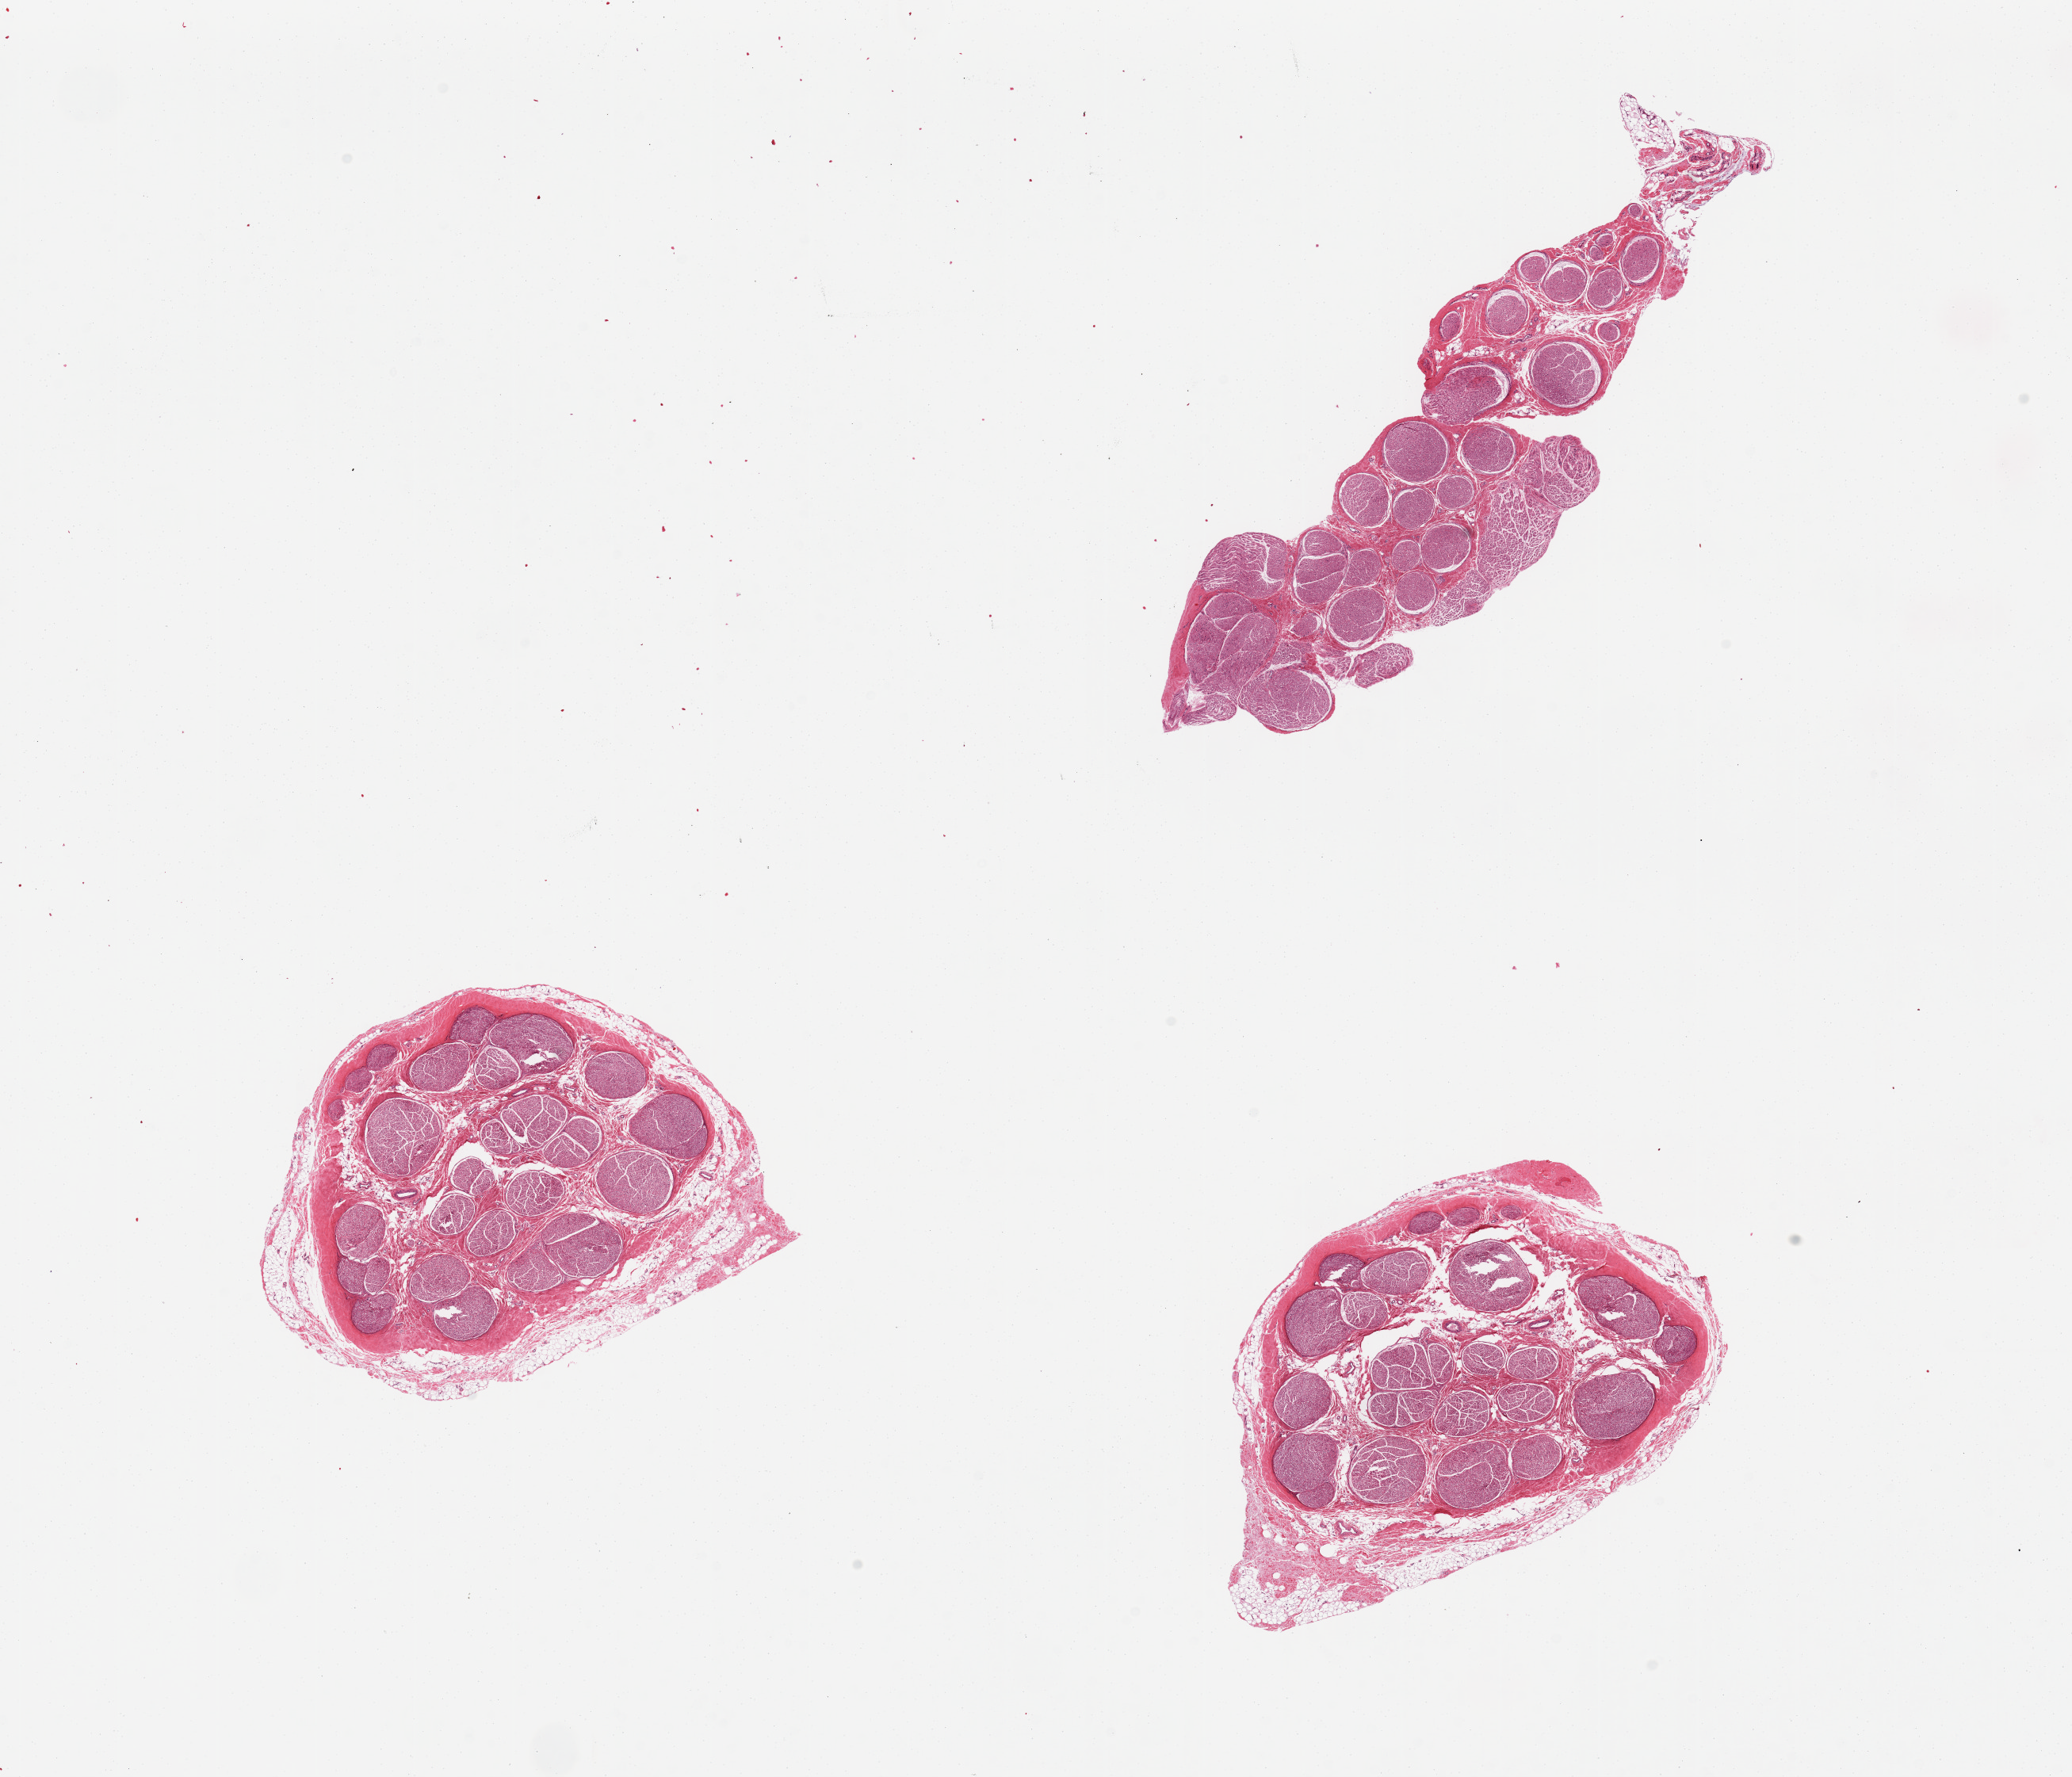
Digitized haematoxylin and eosin-stained section, brightfield, low-resolution overview of the scanned area, about 20.7 x 17.7 mm; PAXgene-fixed paraffin-embedded (PFPE) section; section of tibial nerve (target tissue); donor tissue sample. Donor: male.
* review note (as recorded): 3 pieces, two include peripheral rim of adipose tissue (10-20%)